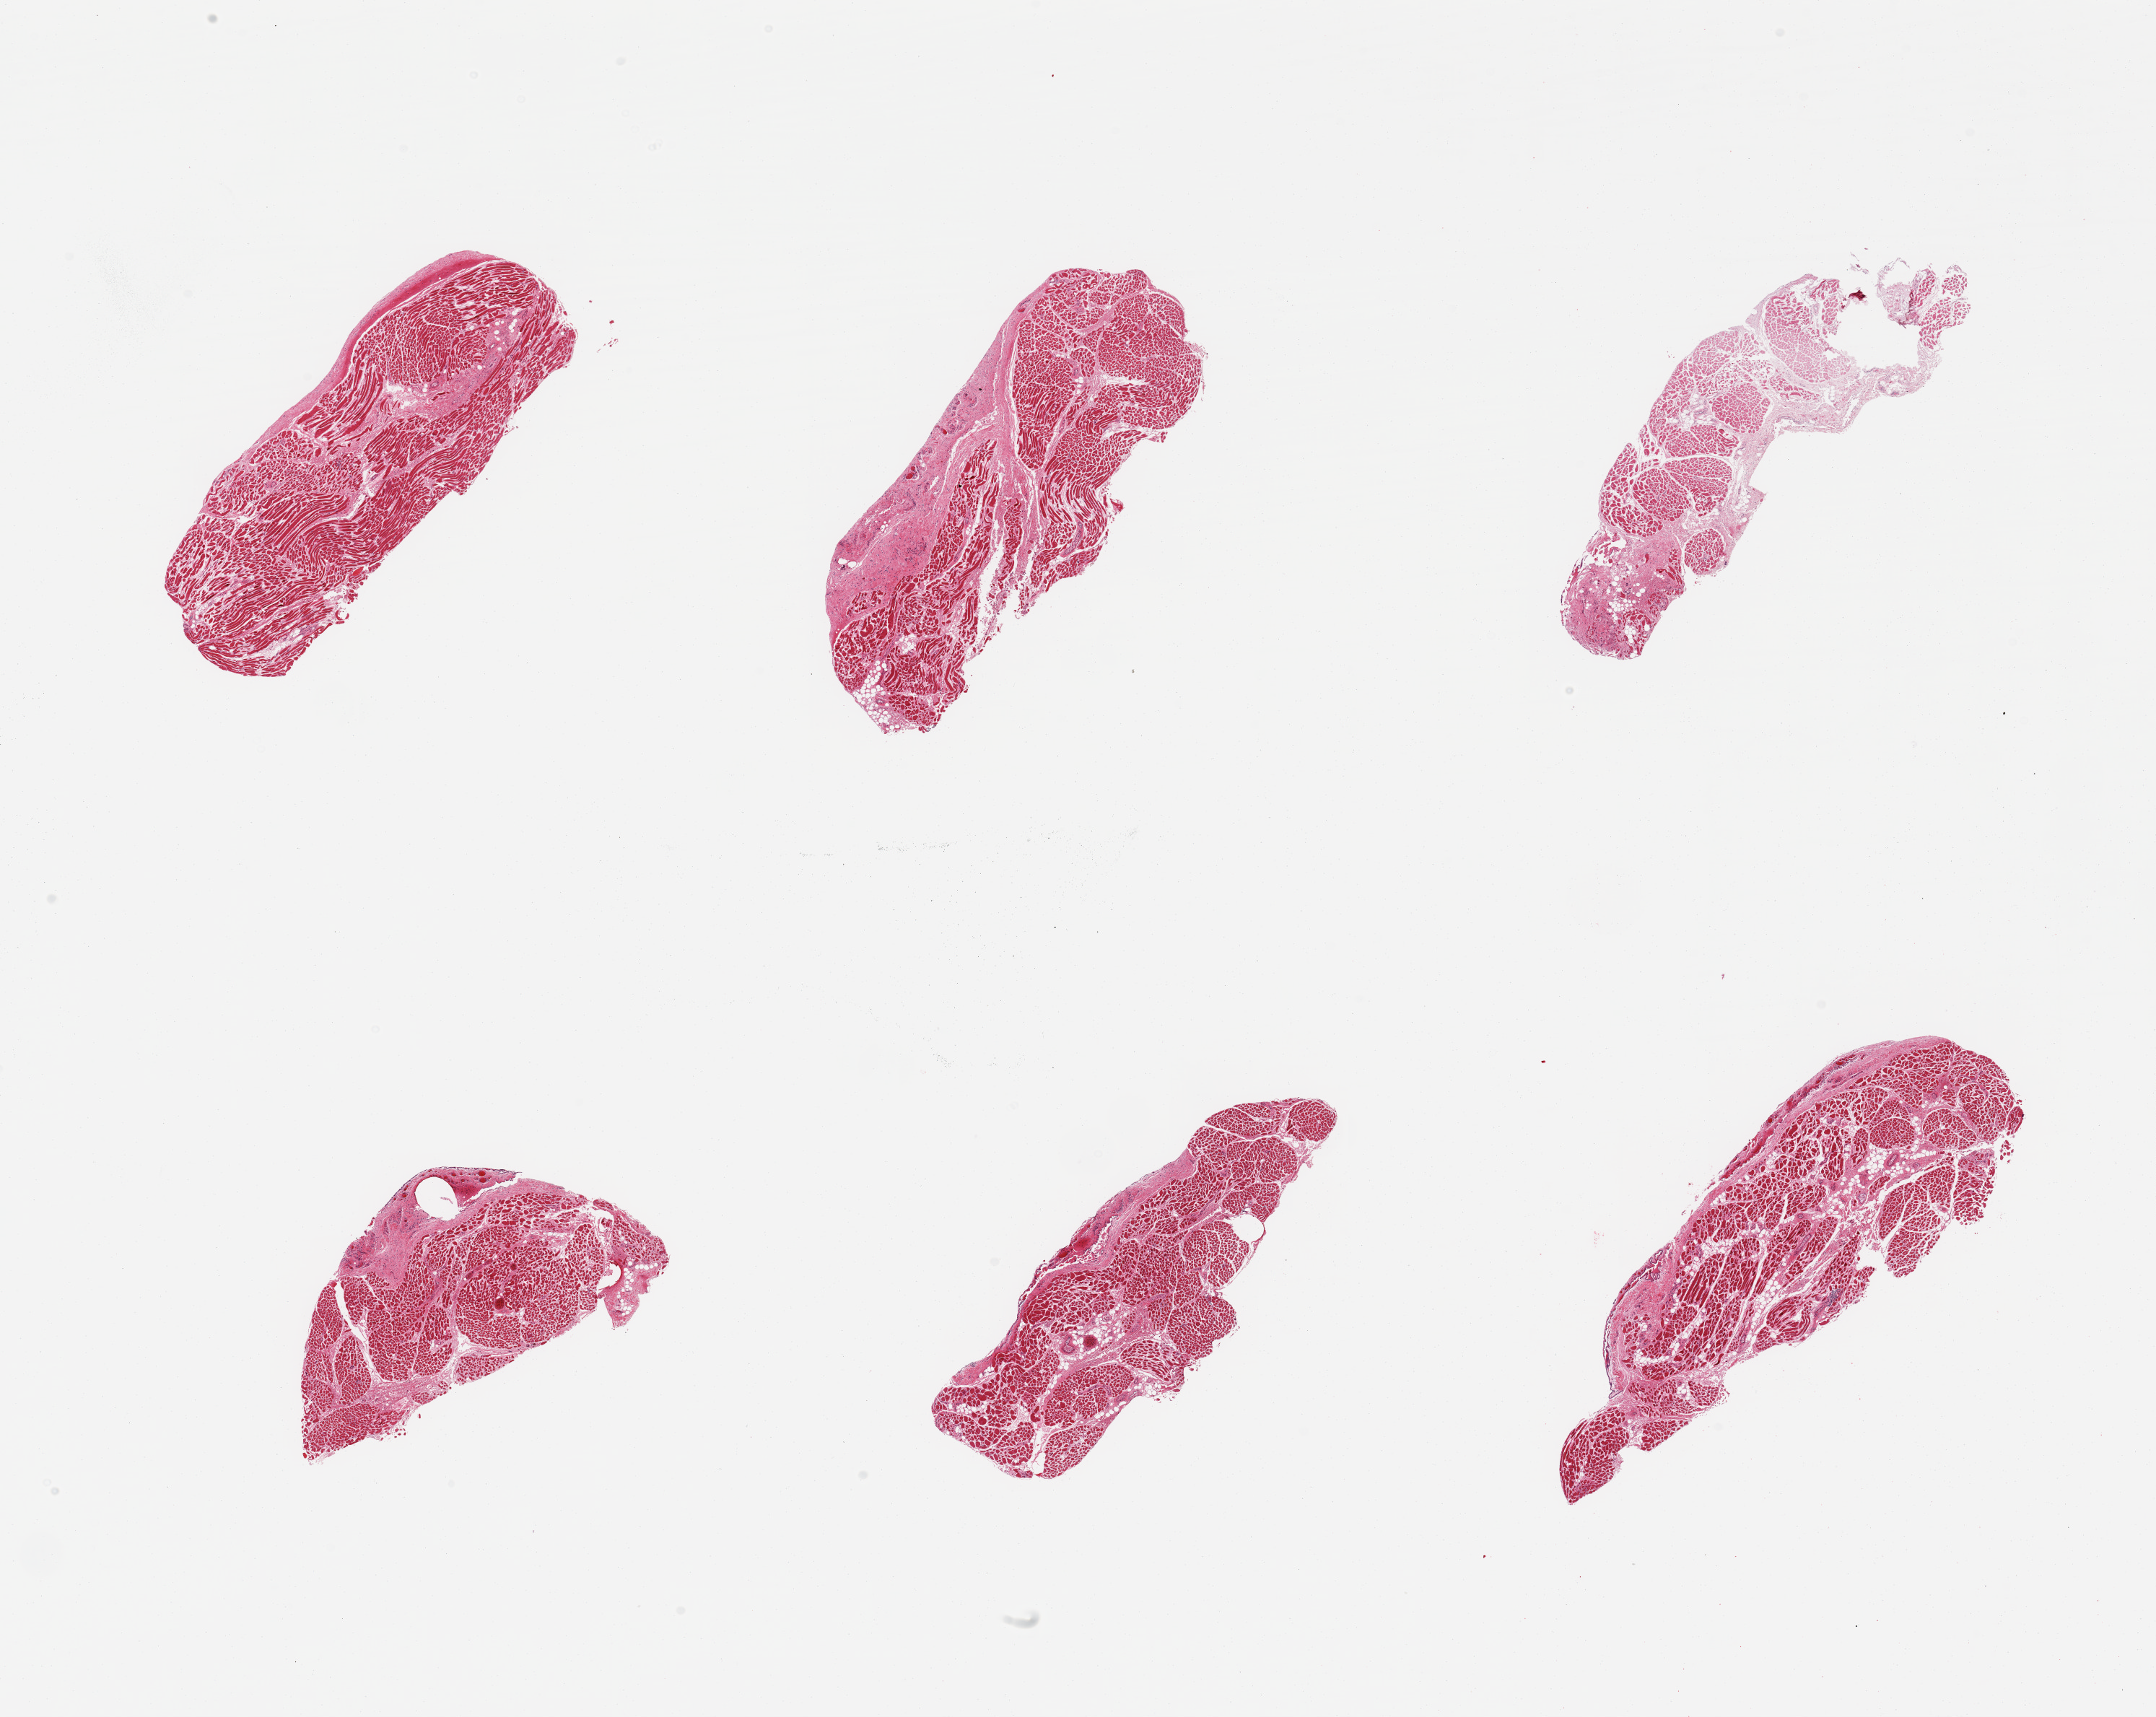
Digitized haematoxylin and eosin-stained section, shown as a low-resolution overview of the whole scanned area (about 23.6 x 18.8 mm), PAXgene-fixed, paraffin-embedded tissue, section of esophageal muscle (target tissue), donor tissue sample.
Reviewer comment on this tissue sample: 6 pieces; skeletal muscle indicating sampling of upper esophagus.